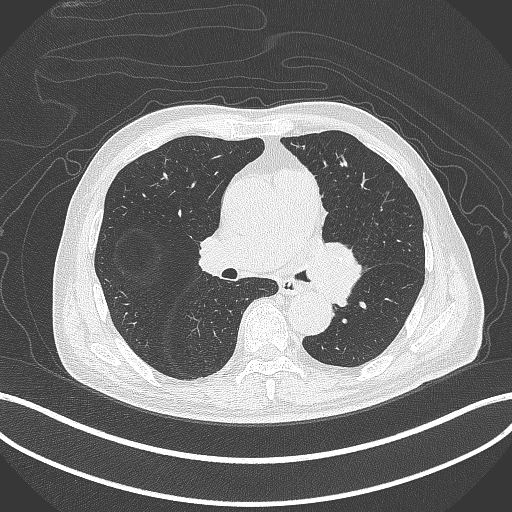
Chest CT, one axial slice; position 242 of 417 along the scan axis; reconstruction kernel B70f; lung window (W 1500 / L -600 HU); 512 × 512 image matrix, field of view 400 × 400 mm. Patient: male, 77 years. Case-level facts recorded for this patient, not image findings: clinical TNM (as recorded): T3 N1 M0.
Annotated regions visible in this slice (bounding box drawn by a radiologist):
- lung tumour (recorded histology: adenocarcinoma): bounding box <308,237,364,310> (left, top, right, bottom; pixels)